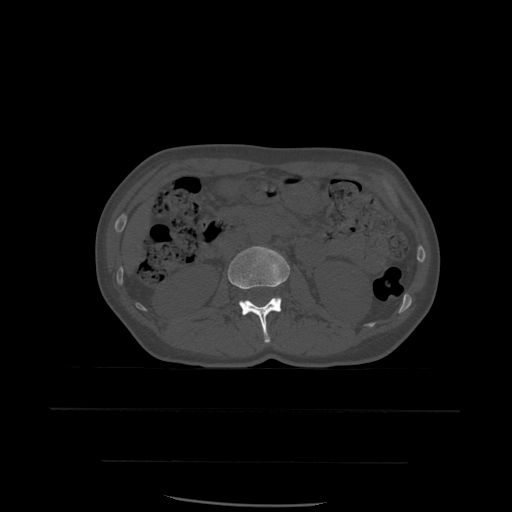
CT including the spine, one axial slice. Position 222 of 574 along the scan axis. Bone window (W 1800 / L 400 HU). 512 × 512 image matrix, field of view 392 × 392 mm. Patient age 48 years. Case-level facts recorded for this patient, not image findings: primary cancer: lung; vertebrae with lytic lesions (as recorded): T11.
Outlined on this slice (semi-automatically segmented with operator editing):
- L2 vertebra: box from (x=228, y=246) to (x=290, y=343) px